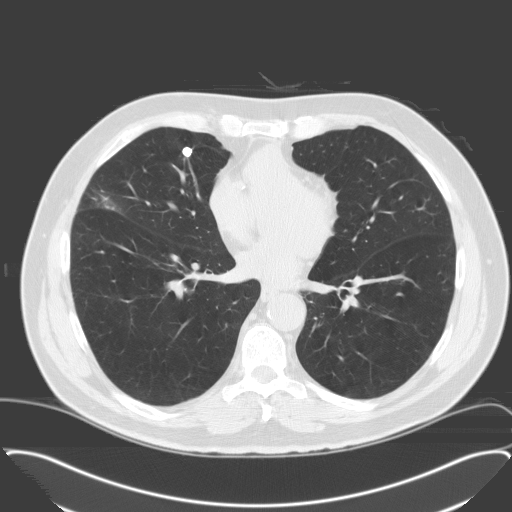
Low-dose screening chest CT, one axial slice; slice 82 of 174 in the series (ordered by position); 120 kVp; lung window (W 1500 / L -600 HU); 3.2 mm slice thickness; 512 × 512 image matrix.
Annotated regions visible in this slice (expert manual segmentation):
- lesion 1 (tumor, middle lobe of right lung): bounding box <95,193,115,209> (left, top, right, bottom; pixels)